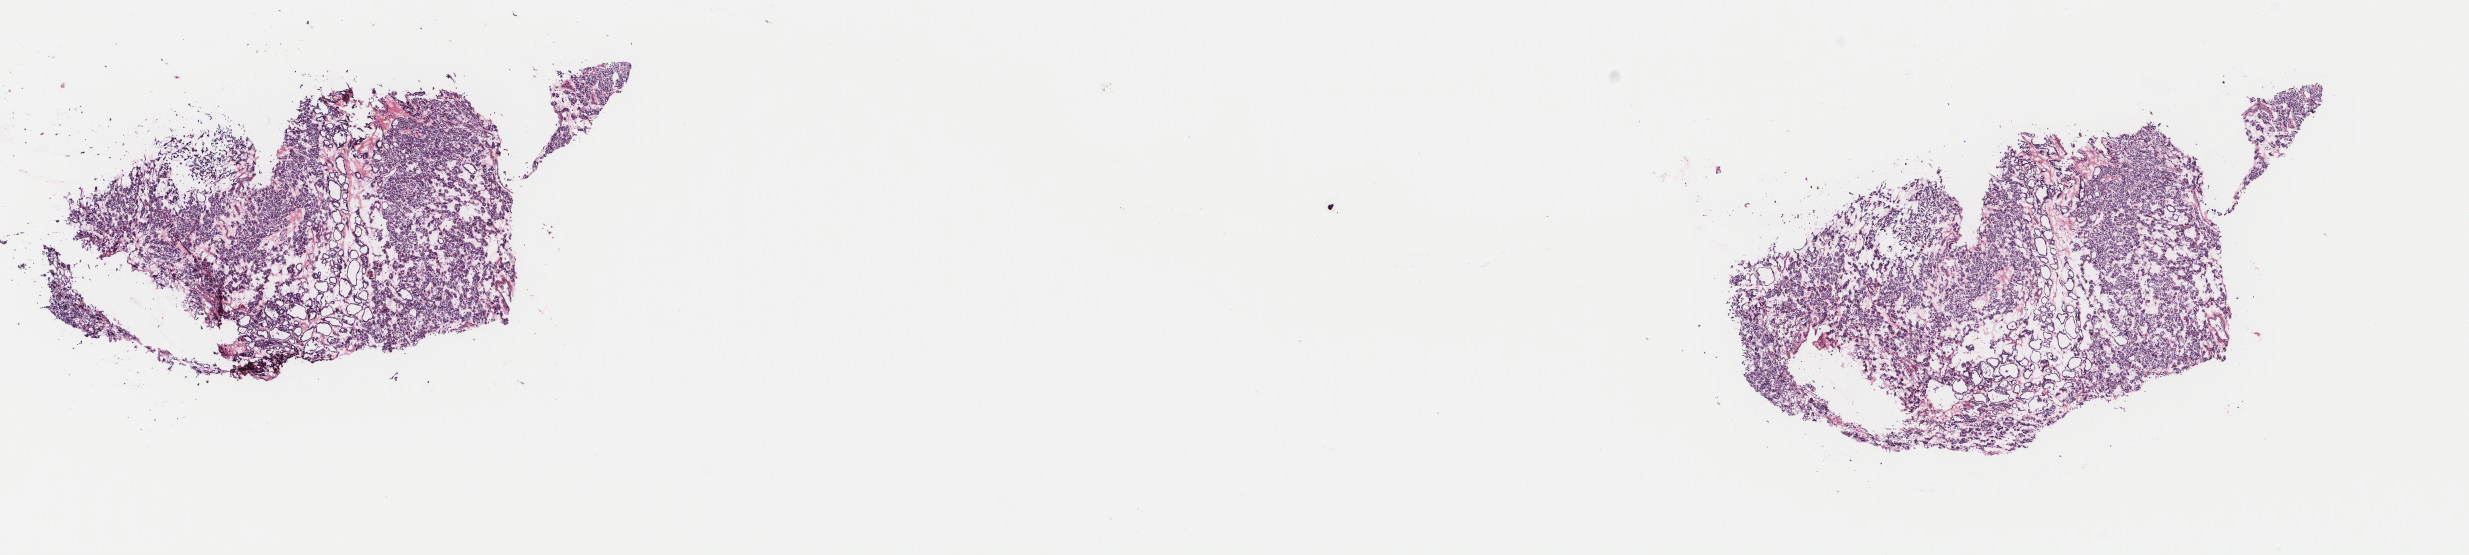
Whole-slide histology image, H&E, a low-resolution overview of the entire scanned area, about 19.6 x 4.4 mm (acquisition: 40x scan). Frozen section from the top of the tissue portion. Primary tumour sample from the thyroid. Male, age 54 years at initial diagnosis.
Diagnosis: Papillary adenocarcinoma, NOS (thyroid gland).